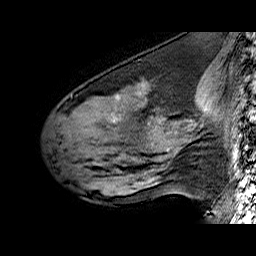
Breast MRI (dynamic contrast-enhanced), one sagittal slice. Position 23 of 60 along the scan axis. Dynamic contrast-enhanced series, time point 2 of 6 at this slice position (early post-contrast). 1.5 T. TE 6.4 ms, TR 32.9 ms. 4 mm slice thickness. 256 × 256 image matrix, field of view 200 × 200 mm. Female patient. From the clinical record (not read from this slice): setting: breast cancer imaged before/during neoadjuvant chemotherapy; receptor status: HER2-positive.
Annotated regions visible in this slice (semi-automatically segmented with operator editing):
- analysis volume of interest (the breast-tissue region the enhancement analysis was run in; not a lesion): bounding box (x1, y1, x2, y2) in pixels: (56, 78, 196, 160)
- tumour enhancement mask (voxels above the 100 % enhancement threshold inside the analysis volume of interest): (113, 95, 169, 150)